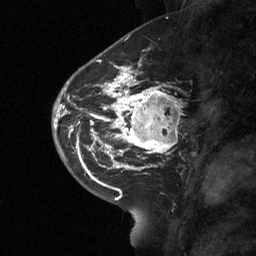
Breast MRI (dynamic contrast-enhanced), one sagittal slice. Position 27 of 64 along the scan axis. Dynamic contrast-enhanced study with each time point stored as its own series, time point 2 of 3 at this slice position (early post-contrast, ordered by acquisition time). 1.5 T. TE 4.8 ms, TR 27 ms. 2 mm slice thickness. 256 × 256 image matrix, field of view 180 × 180 mm. Female patient, age 42 years. From the clinical record (not read from this slice): setting: breast cancer imaged before/during neoadjuvant chemotherapy; receptor status: triple-negative.
Outlined on this slice (semi-automatically segmented with operator editing):
- analysis volume of interest (the breast-tissue region the enhancement analysis was run in; not a lesion): bounding box (x1, y1, x2, y2) in pixels: (115, 85, 178, 160)
- tumour enhancement mask (voxels above the 90 % enhancement threshold inside the analysis volume of interest): (115, 85, 177, 157)